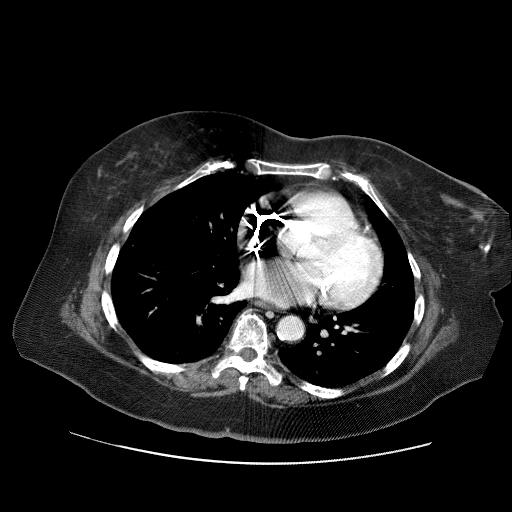
Contrast-enhanced abdominal CT (liver protocol), one axial slice. Position 68 of 71 along the scan axis. Reconstruction kernel STANDARD. Soft-tissue window (W 400 / L 40 HU). 2.5 mm slice thickness. 512 × 512 image matrix, field of view 400 × 400 mm. From the clinical record (not read from this slice): diagnosis: hepatocellular carcinoma (patient treated with transarterial chemoembolisation; whether this scan precedes or follows treatment is not stated here); TNM stage (as recorded): Stage-II; Child-Pugh class: A; tumour nodularity: multinodular; tumour size: 5 cm.
Outlined on this slice (semi-automatically segmented with operator editing):
- abdominal aorta: bounding box [x1, y1, x2, y2] px = [278, 317, 303, 339]